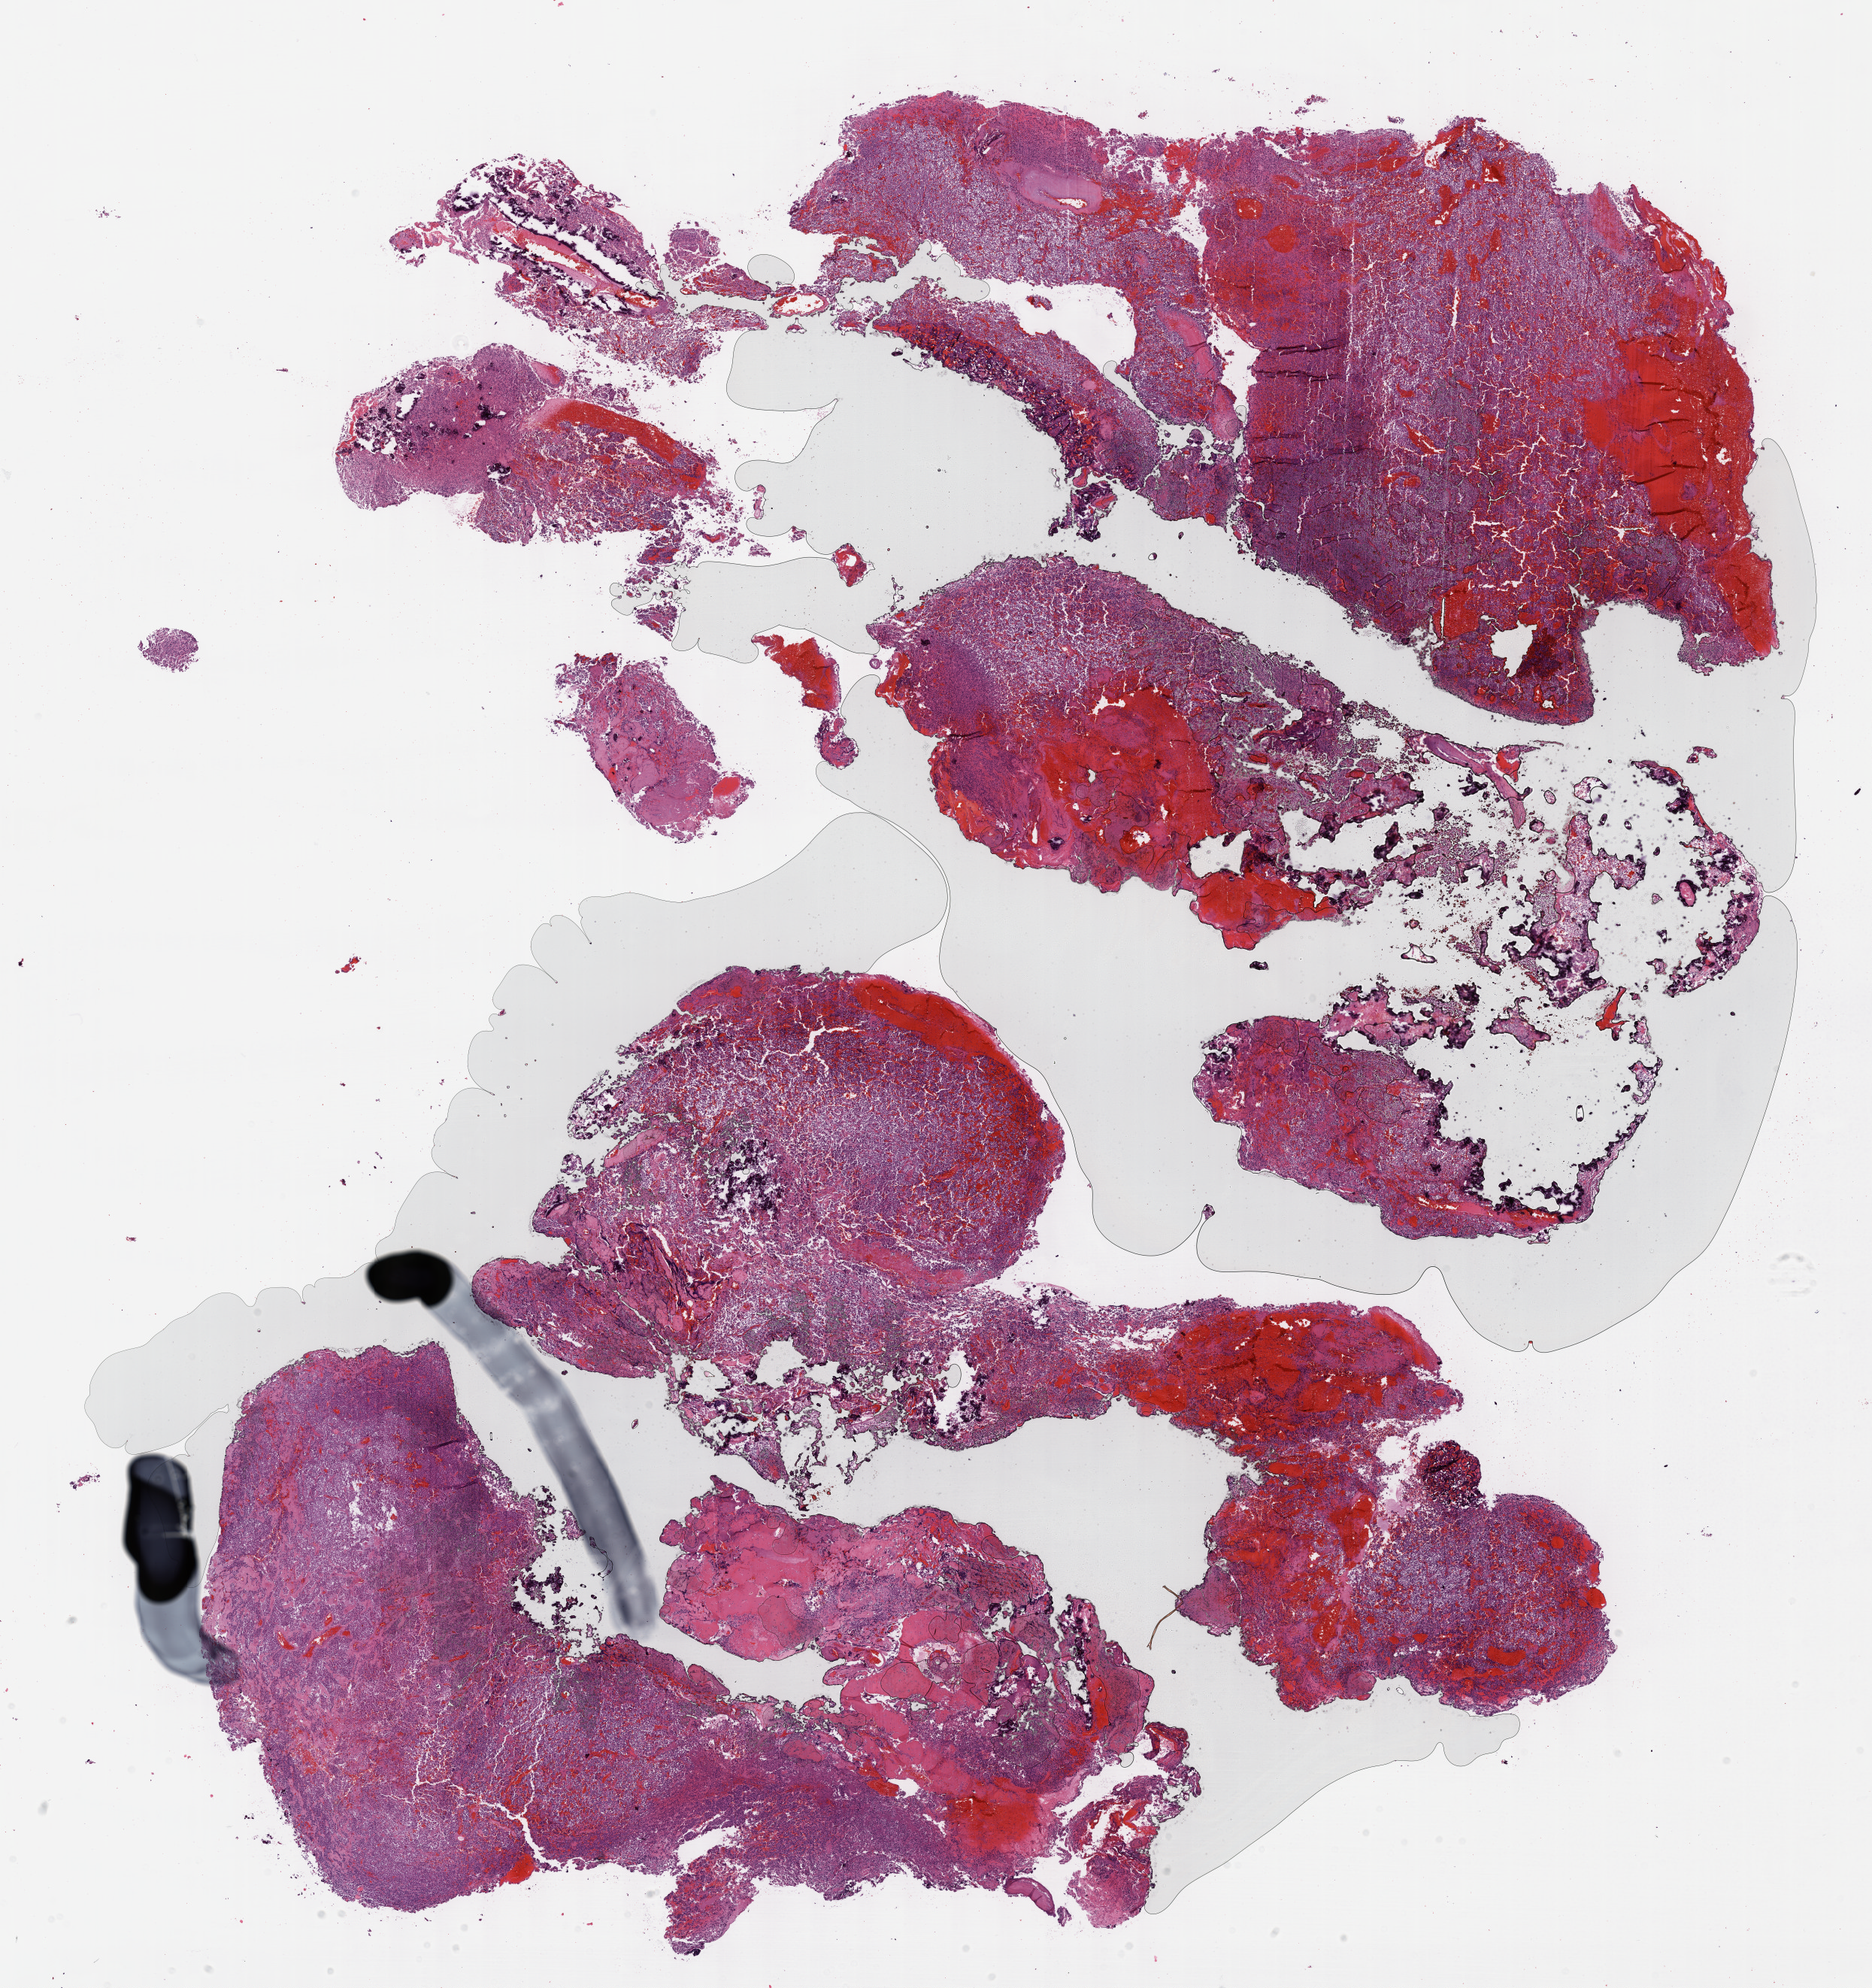
H&E-stained whole-slide image — whole scanned area (about 20.1 x 21.4 mm, slide scanned at 40x) shown as a low-resolution overview; formalin-fixed paraffin-embedded (FFPE) diagnostic section; brain, primary tumour sample. Female patient; age at initial diagnosis 51 years. Histologic grade: G3 (poorly differentiated).
Histologic diagnosis: Oligodendroglioma, anaplastic (cerebrum).